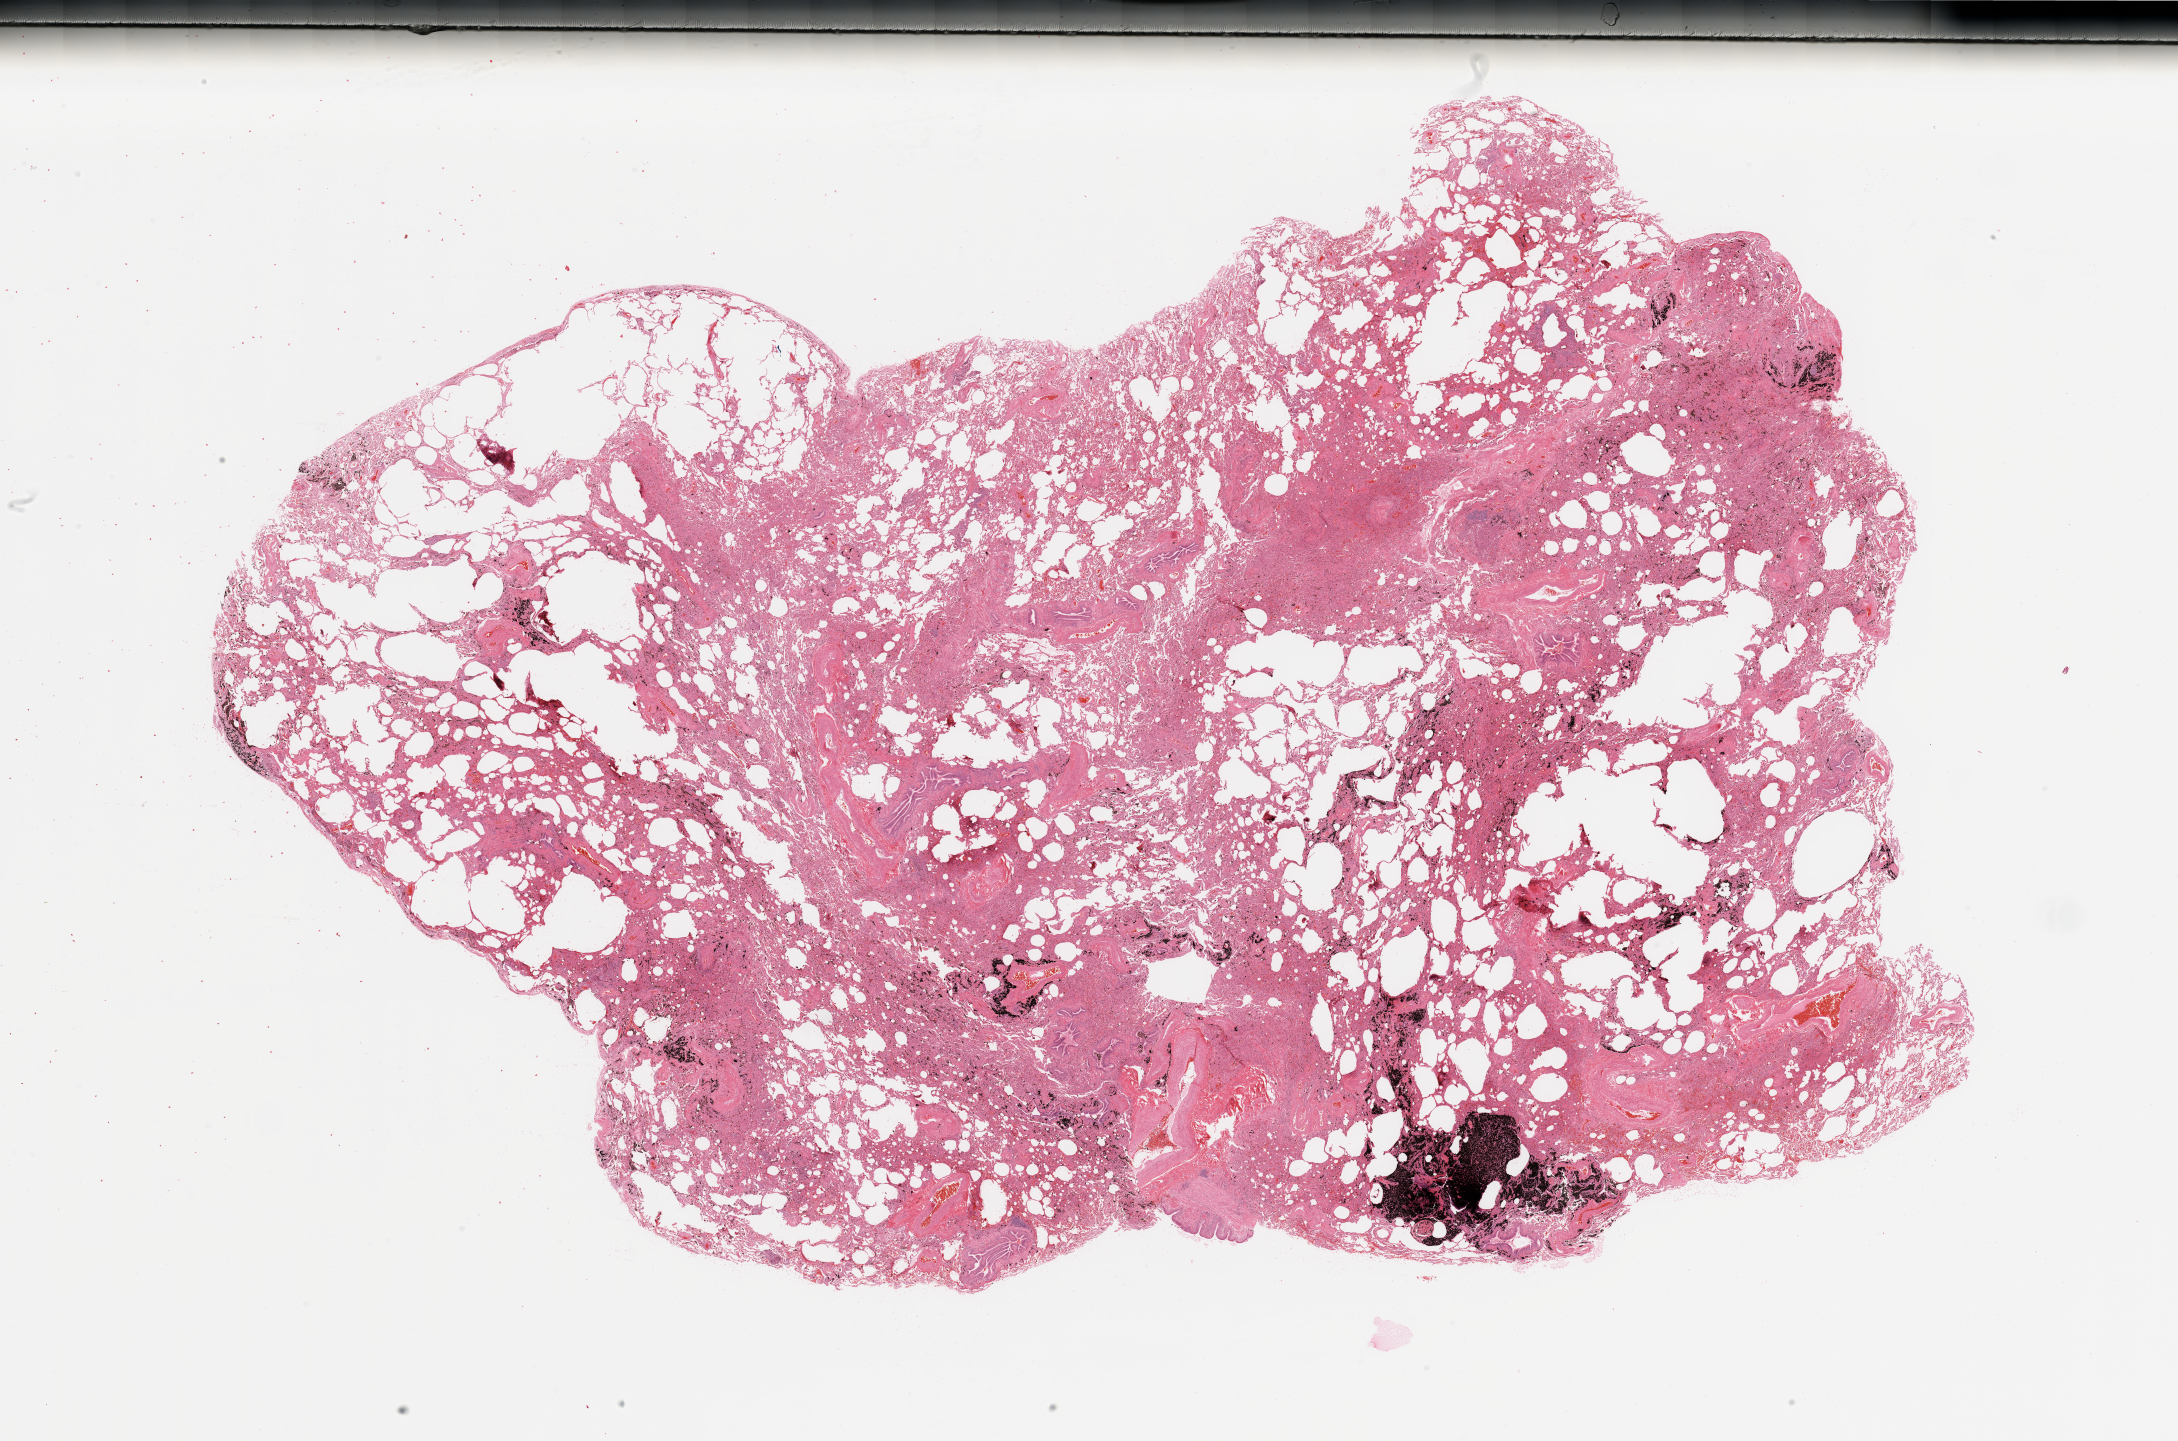
Hematoxylin and eosin (H&E) stained whole-slide image — whole scanned area (about 34.5 x 22.8 mm) shown as a low-resolution overview, lung, normal (non-tumour) tissue. 57-year-old male patient.
- this section: normal (non-tumour) tissue from the same patient
- patient diagnosis: Adenocarcinoma, NOS